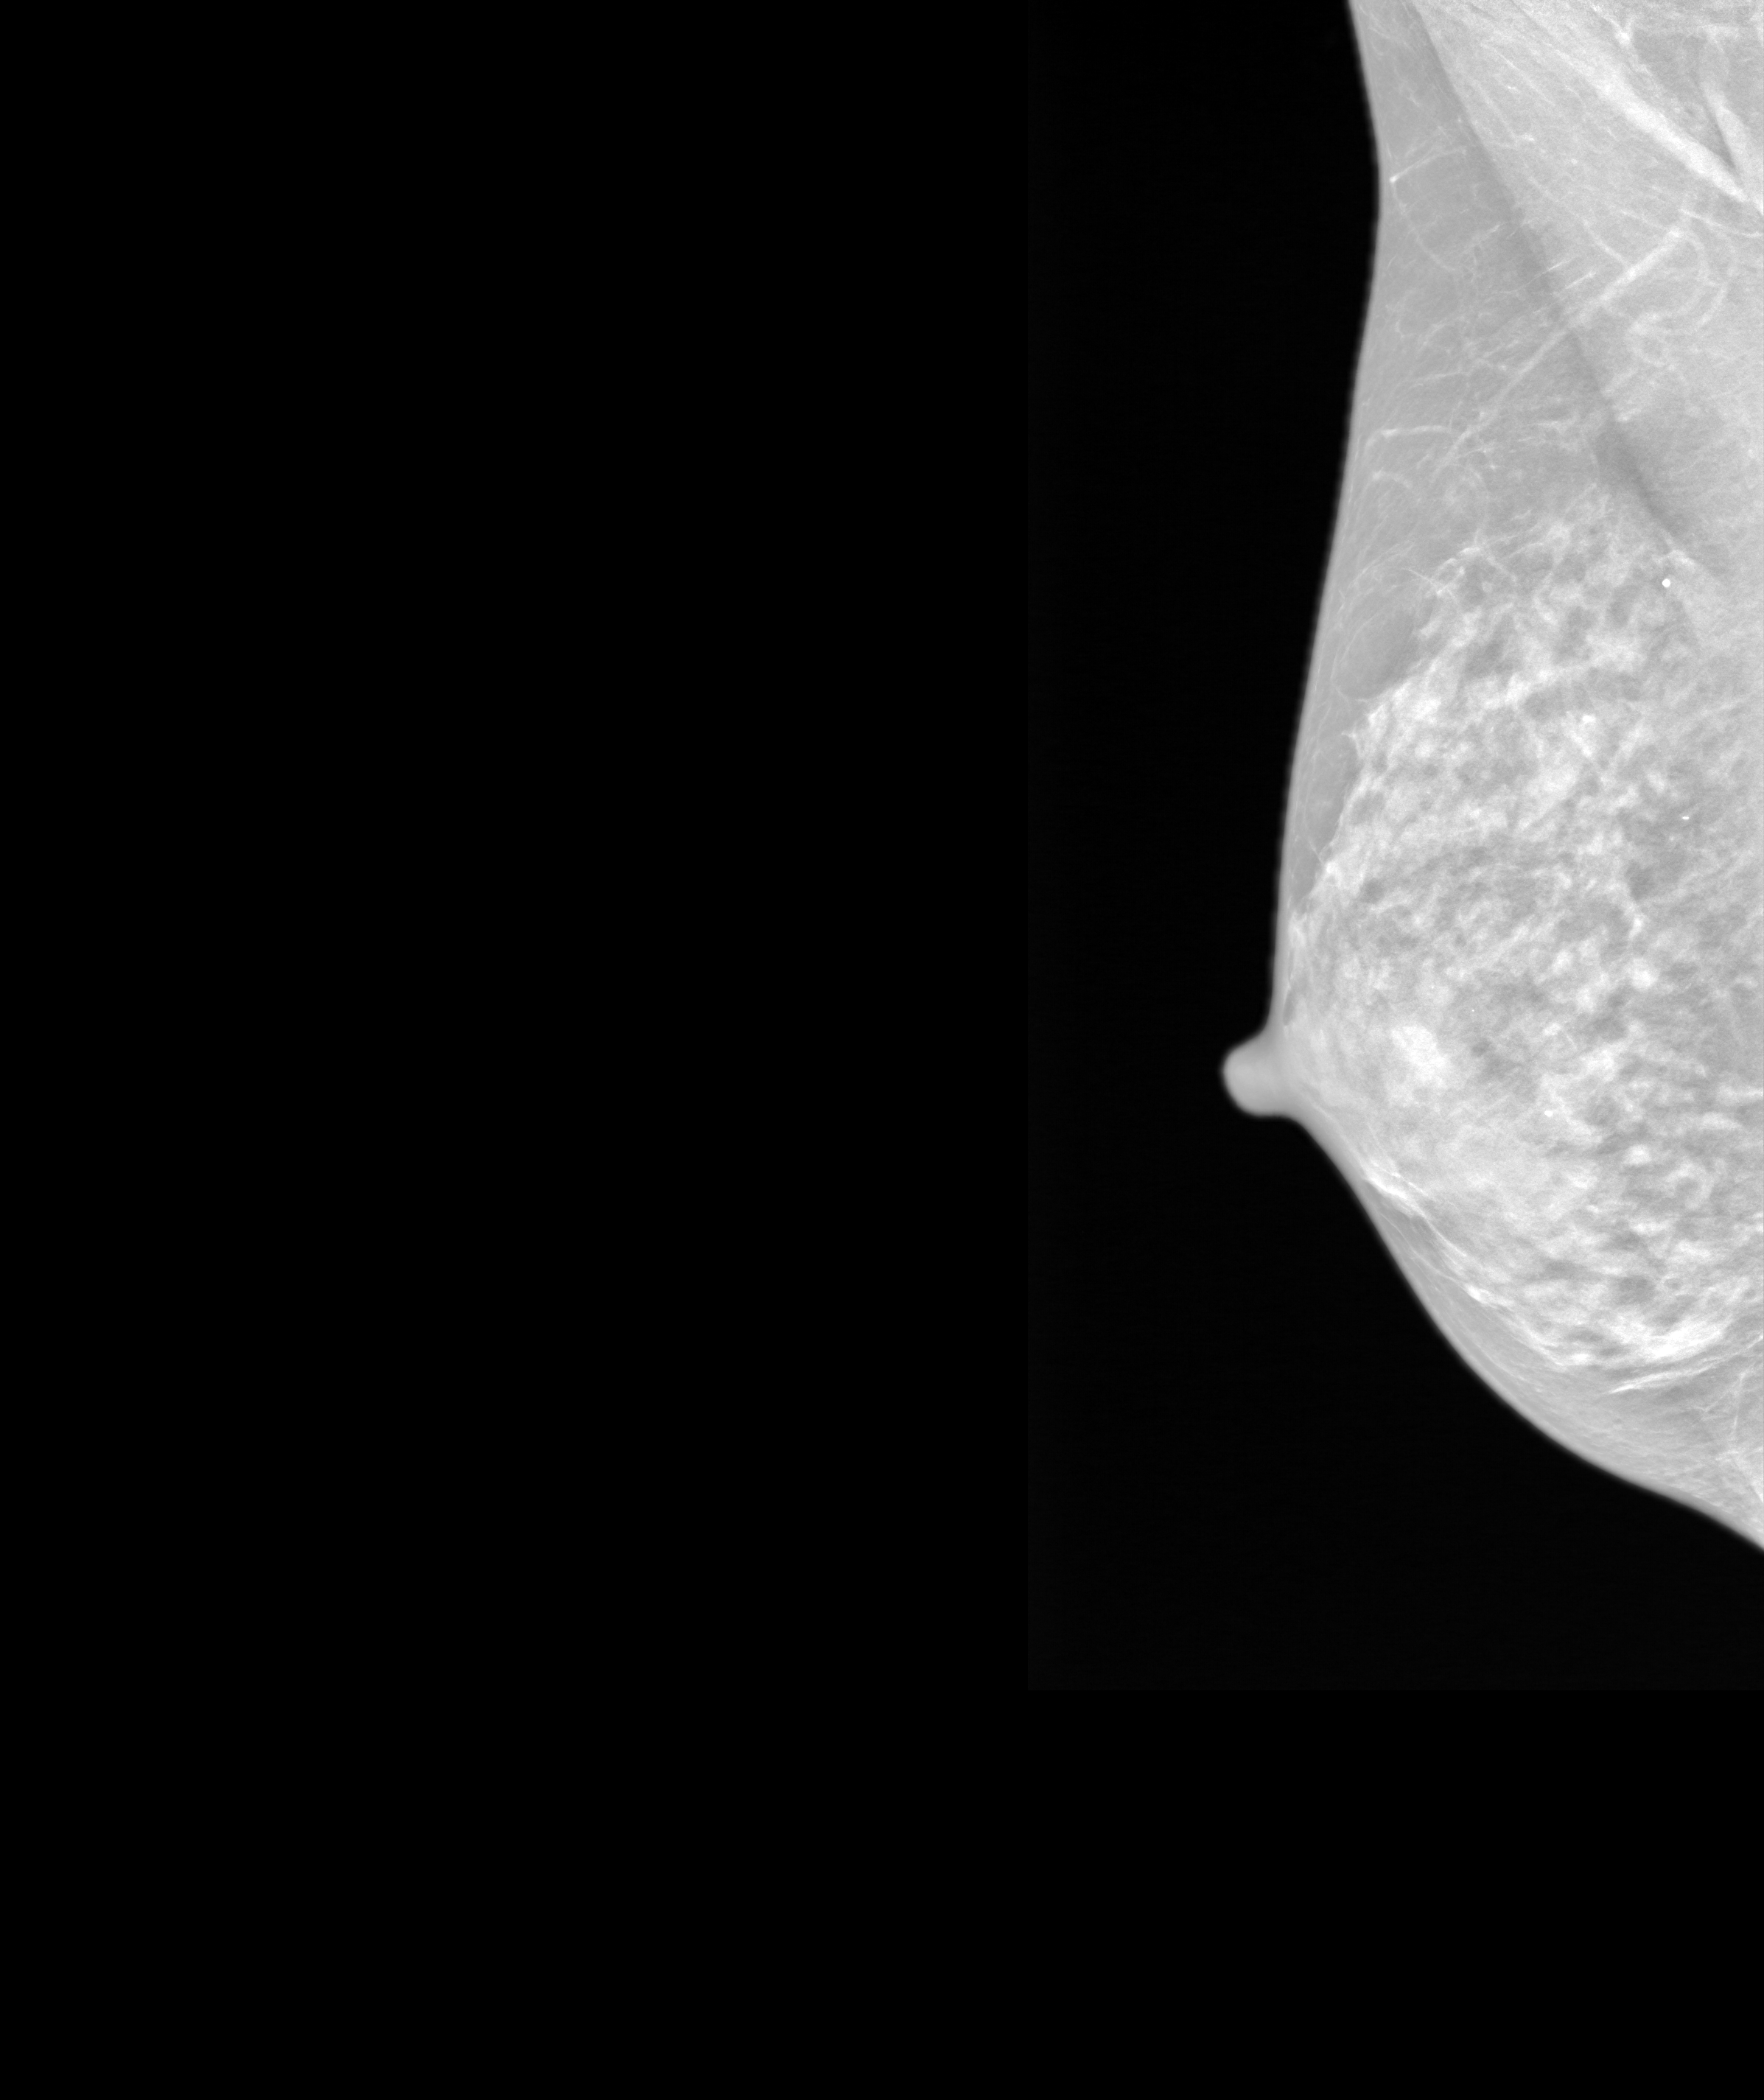
Annual screening mammography examination, system: SenoIris_1SP2(440). Patient aged 68 years (female).
Image type: synthesized 2-D view from tomosynthesis. Breast: right. Projection: medio-lateral oblique projection.